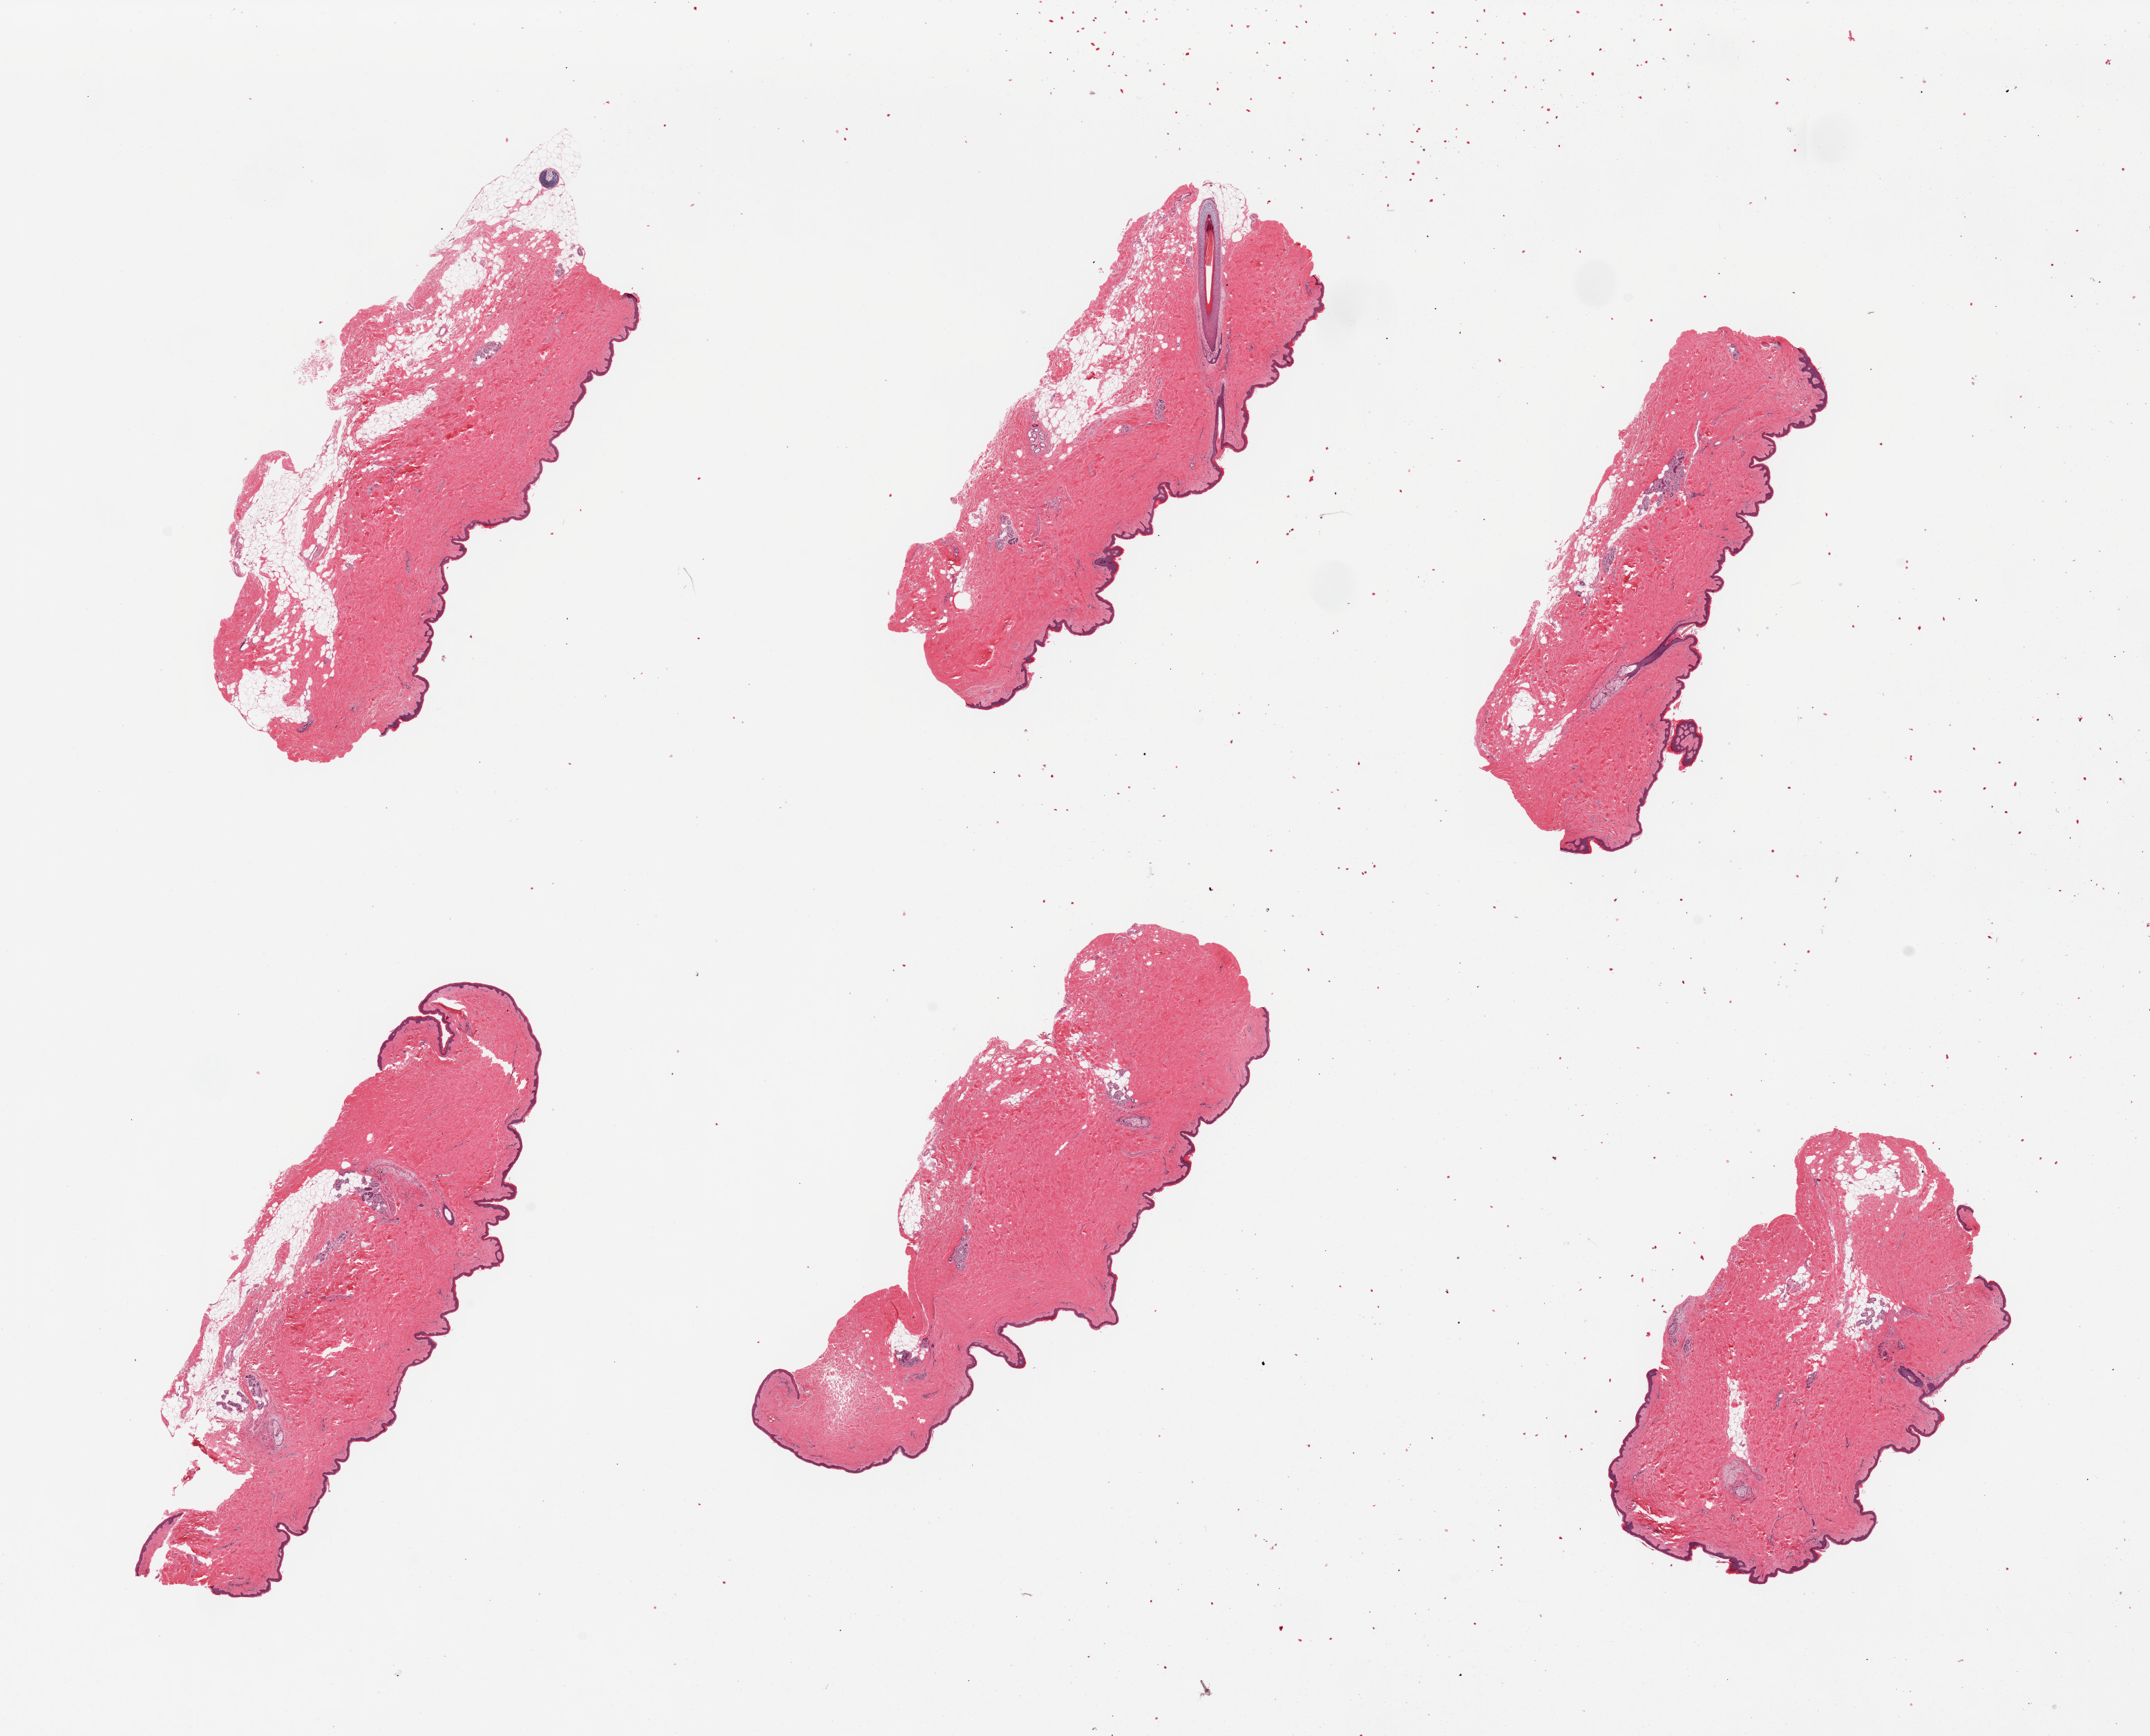
Haematoxylin and eosin whole-slide image, low-resolution overview of the scanned area, about 24.6 x 19.9 mm (slide scanned at 20x). PAXgene-fixed paraffin-embedded (PFPE) section. Target tissue: skin of suprapubic region. Tissue donor sample. Male donor.
* pathologist's review note for this sample: 6 pieces. internal fat up to 0.7mm in all